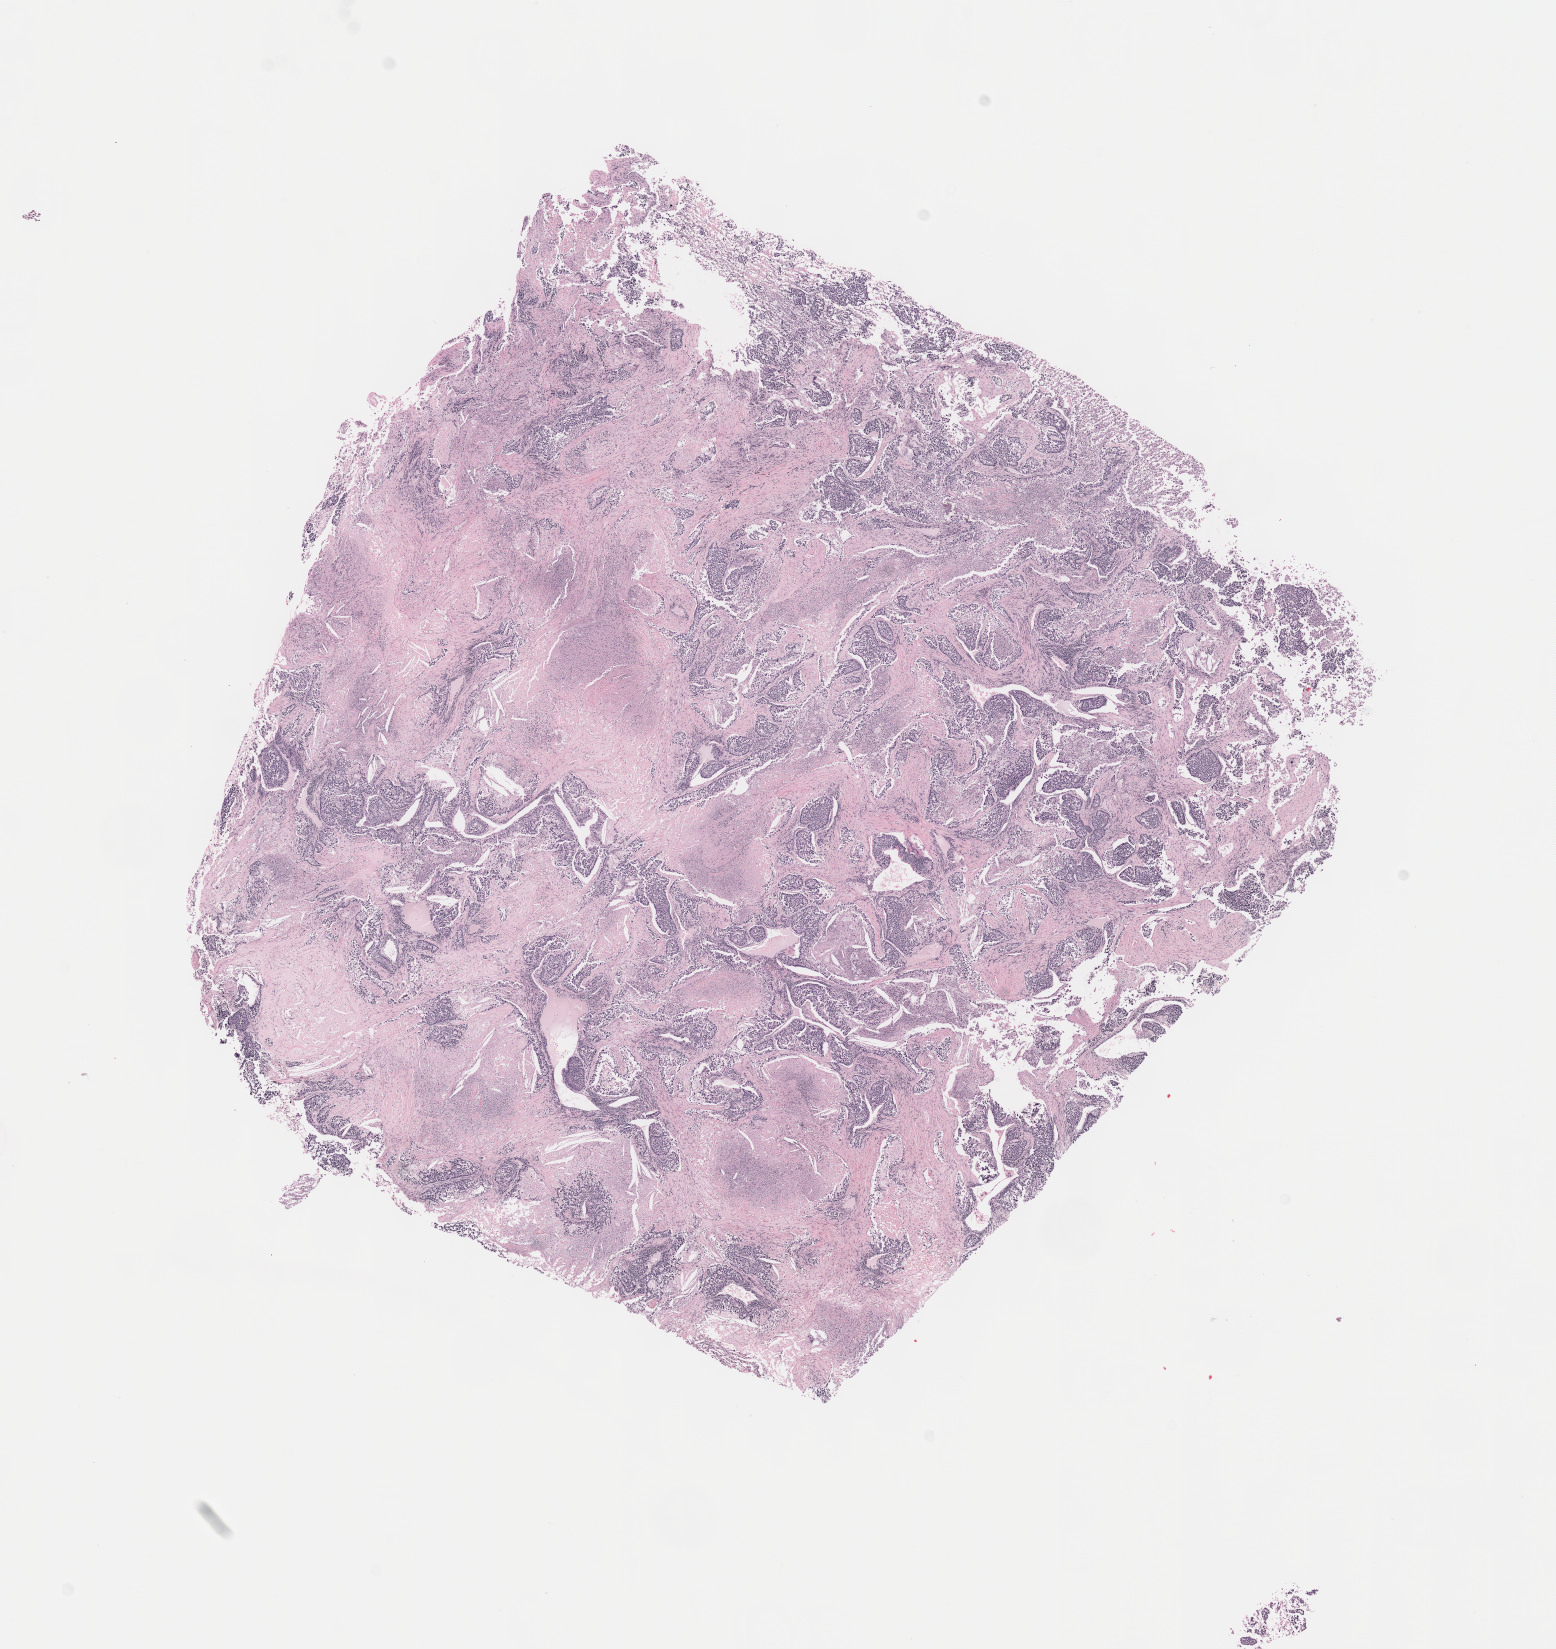
Whole-slide histology image, Hematoxylin and eosin (H&E) stained, low-resolution overview of the scanned area, about 12.6 x 13.3 mm (slide scanned at 40x), formalin-fixed paraffin-embedded (FFPE) diagnostic section, sample: primary tumour, lung. Patient: male, age at initial diagnosis 60 years.
Diagnosis: Adenocarcinoma, NOS (main bronchus).